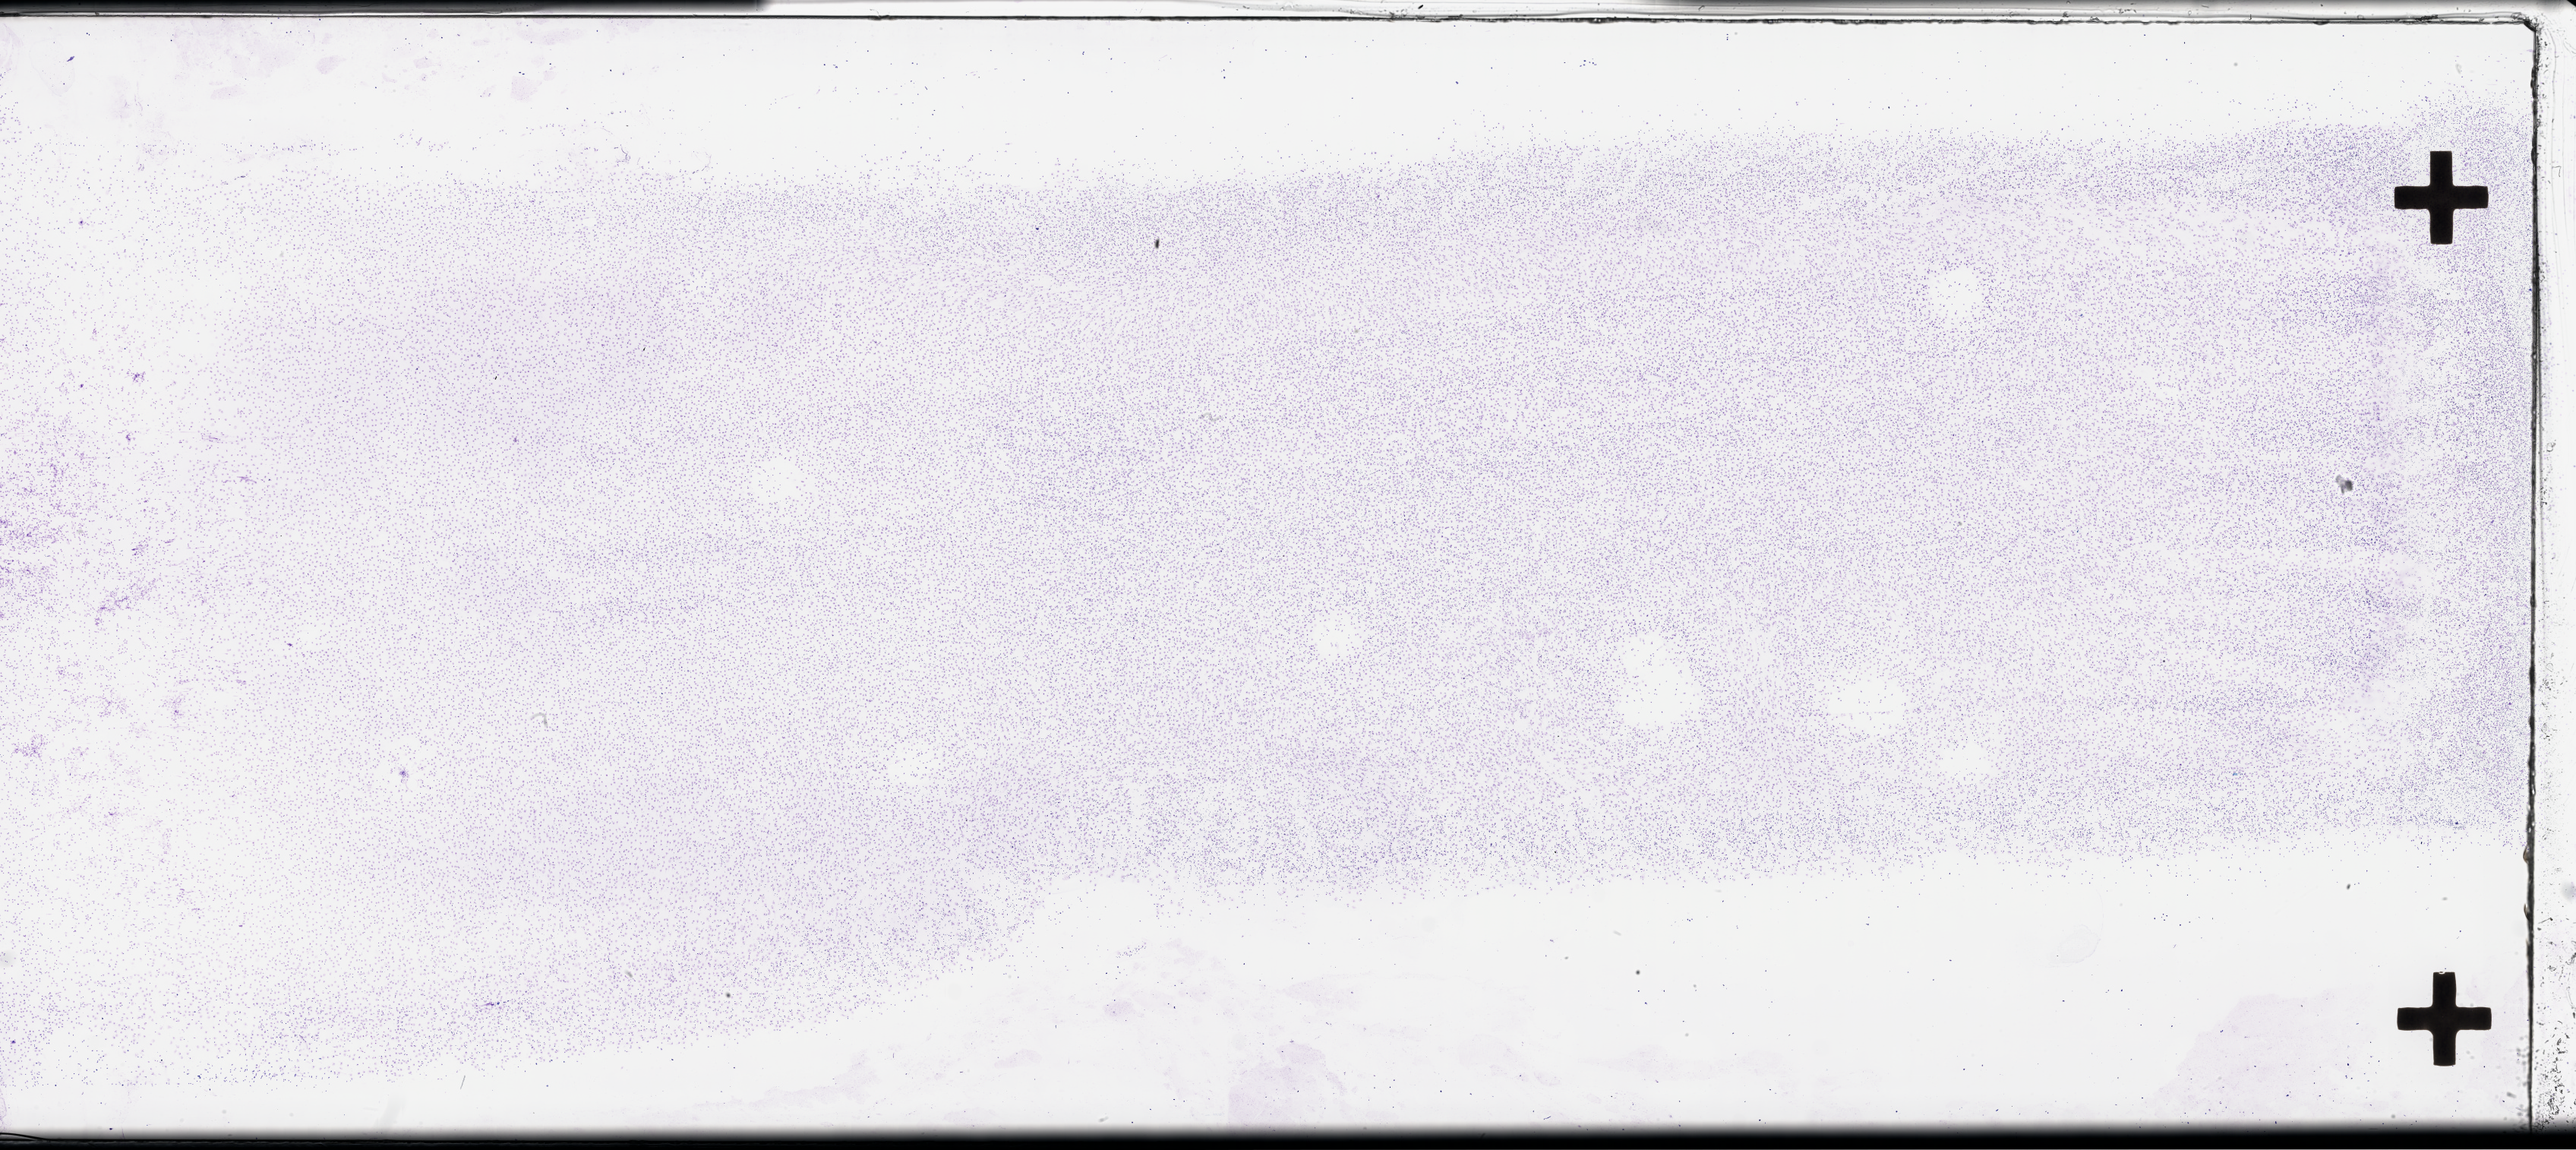
H&E-stained whole-slide image, shown as a low-resolution overview of the whole scanned area (about 54.8 x 24.5 mm). Bone marrow (leukaemic) sample. Blasts: 70%.
- FAB classification: M4
- diagnosis: Acute Myeloid Leukemia